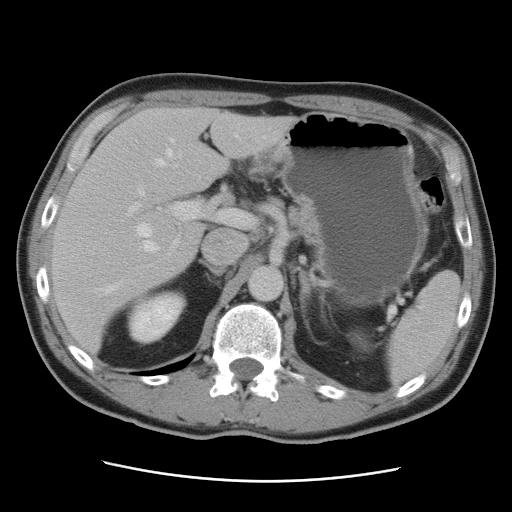
Contrast-enhanced abdominal CT, one axial slice. Position 56 of 89 along the scan axis. Intravenous contrast given. Soft-tissue window (W 400 / L 40 HU). 5 mm slice thickness. 512 × 512 image matrix, field of view 366 × 366 mm. Male patient, age 59 years. From the clinical record (not read from this slice): diagnosis: colorectal cancer liver metastases, imaged before liver resection; multiple liver metastases: yes; largest metastasis: 0.6 cm; disease in both lobes: yes.
Outlined on this slice (manually delineated by an expert):
- hepatic veins: bounding box <95,135,239,294> (left, top, right, bottom; pixels)
- liver: <52,108,293,354>
- planned liver remnant (the part of the liver to remain after resection): <74,107,235,238>
- portal vein (with intrahepatic branches): <127,188,250,271>